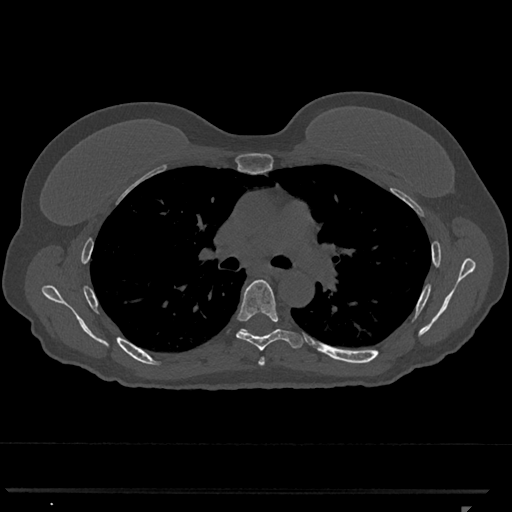
CT including the spine, one axial slice. Slice 760 of 793 in the series (ordered by position). Reconstruction kernel Br40s/3. 120 kVp. Bone window (W 1800 / L 400 HU). 512 × 512 image matrix, field of view 380 × 380 mm. Female patient, age 62 years. From the clinical record (not read from this slice): primary cancer: renal.
Annotated regions visible in this slice (semi-automatic segmentation, software-assisted and operator-edited):
- T5 vertebra: bounding box [x1, y1, x2, y2] px = [259, 358, 265, 366]
- T6 vertebra: [236, 279, 302, 351]